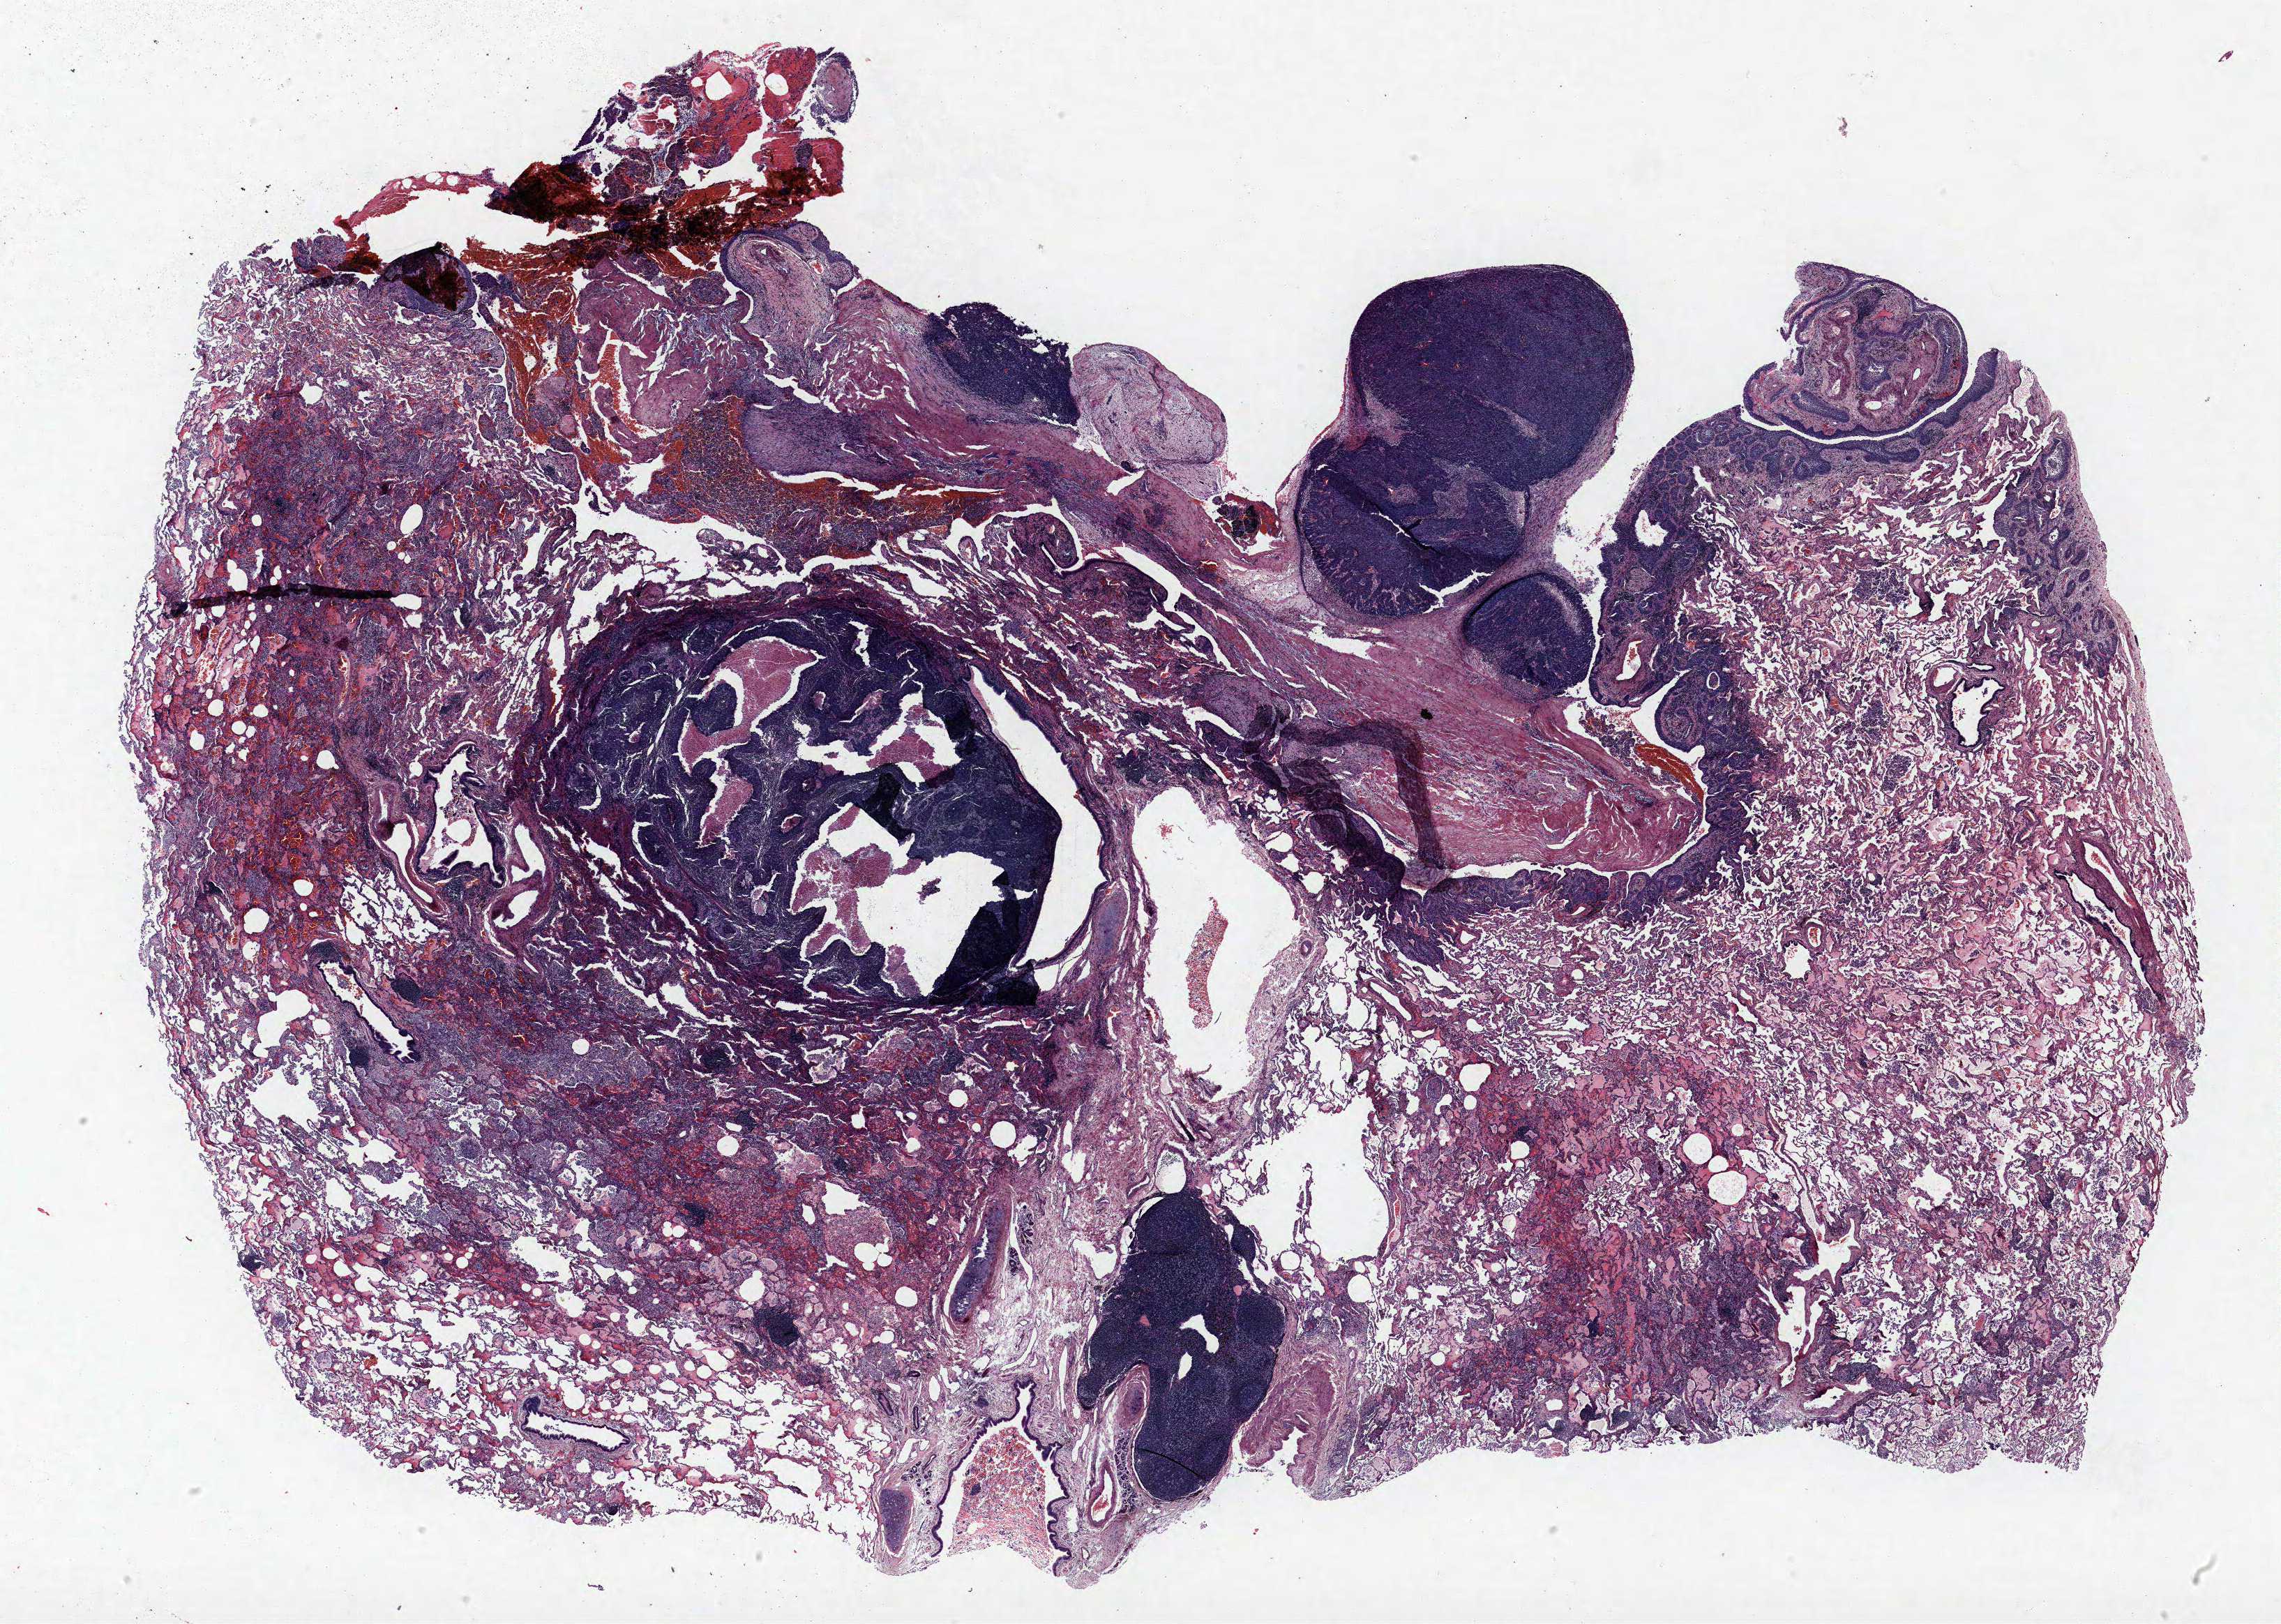
H&E-stained whole-slide image — low-resolution overview of the scanned area, about 26.2 x 18.6 mm (acquisition: 40x scan). Formalin-fixed paraffin-embedded (FFPE) section. Lung tissue. Female, age 69 at enrolment. Grade: poorly differentiated (G3).
Primary tumour location (clinical record): right lower lobe. Tumour size (pathology): 36 mm. Stage (AJCC 6th edition): IB. Participant's lung-cancer diagnosis: Non-small cell carcinoma (ICD-O-3 8046/3).